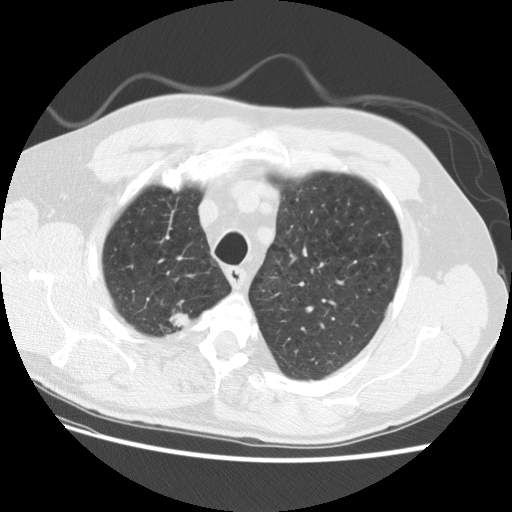
Low-dose screening chest CT, one axial slice. Position 102 of 124 along the scan axis. Lung window (W 1500 / L -600 HU). 2.5 mm slice thickness. 512 × 512 image matrix.
Annotated regions visible in this slice (expert manual segmentation):
- lesion 1 (tumor, upper lobe of right lung): bounding box [x1, y1, x2, y2] px = [169, 300, 195, 328]